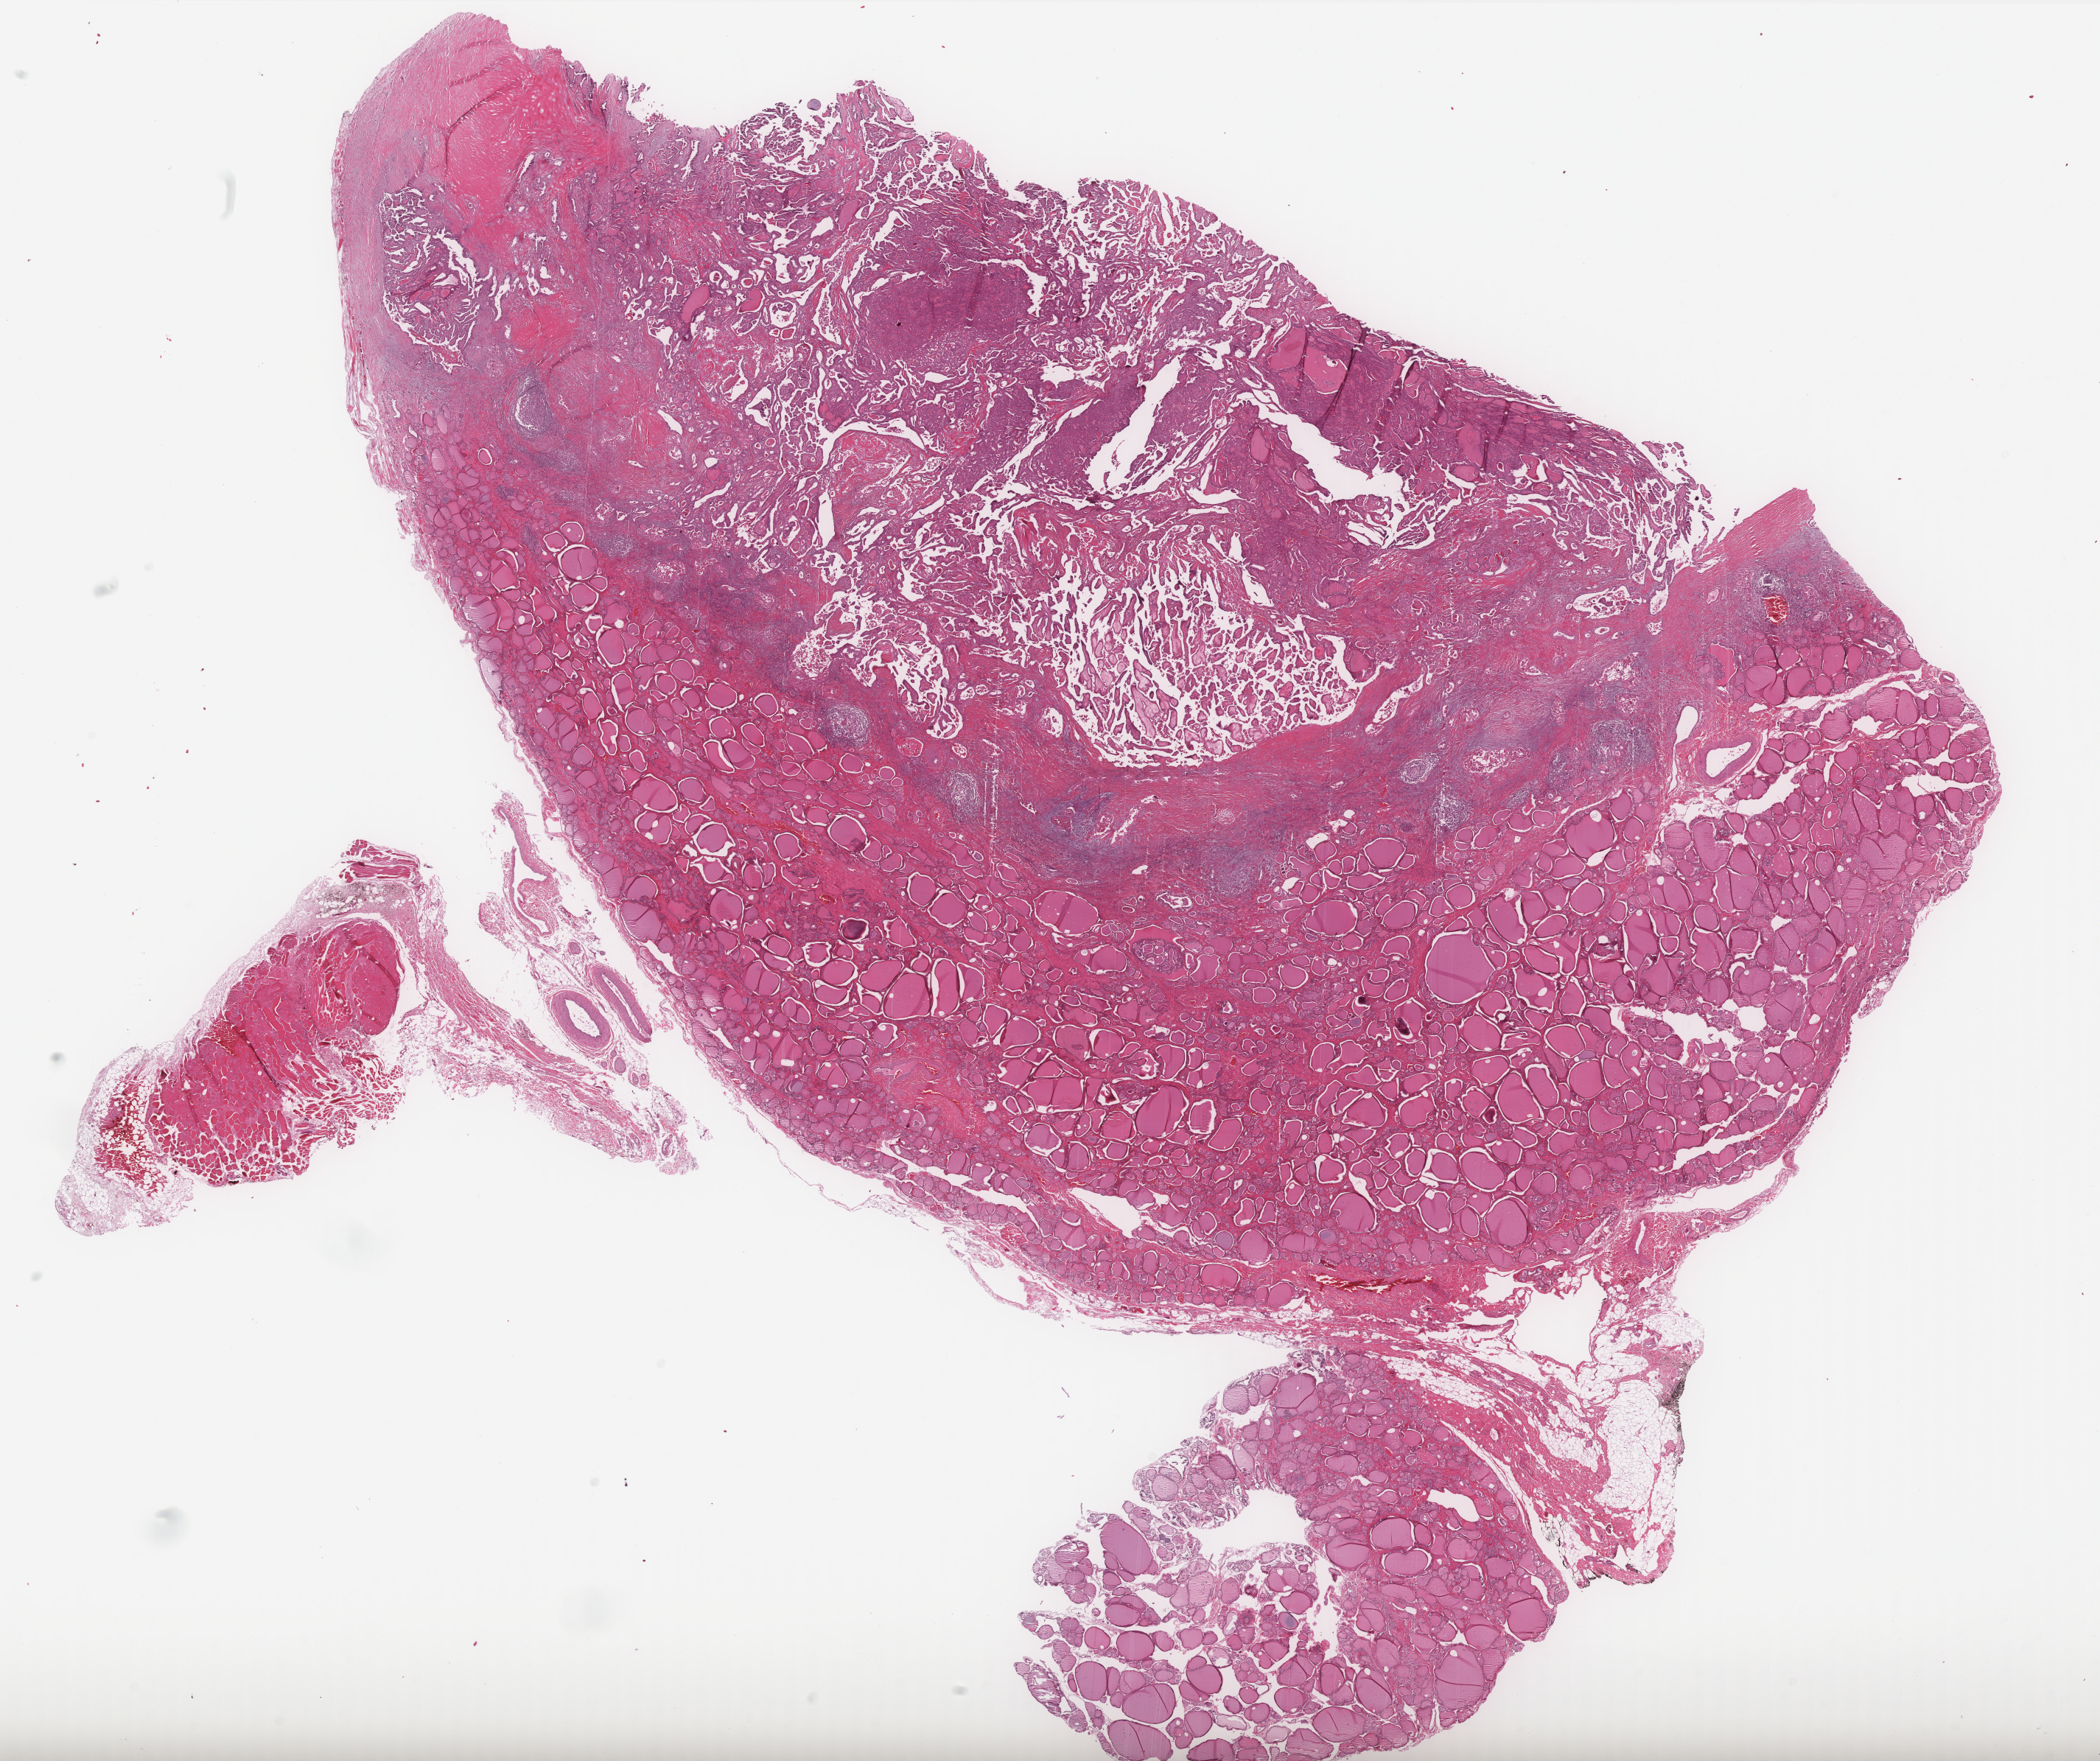
Whole-slide histology image, Hematoxylin and eosin (H&E) stained — low-resolution overview of the scanned area, about 22.8 x 19.2 mm (acquisition: 40x scan), formalin-fixed paraffin-embedded (FFPE) diagnostic section, thyroid, primary tumour sample. Female, age 61 years at initial diagnosis.
* AJCC pathologic stage: III (6th edition)
* histologic diagnosis: Papillary adenocarcinoma, NOS